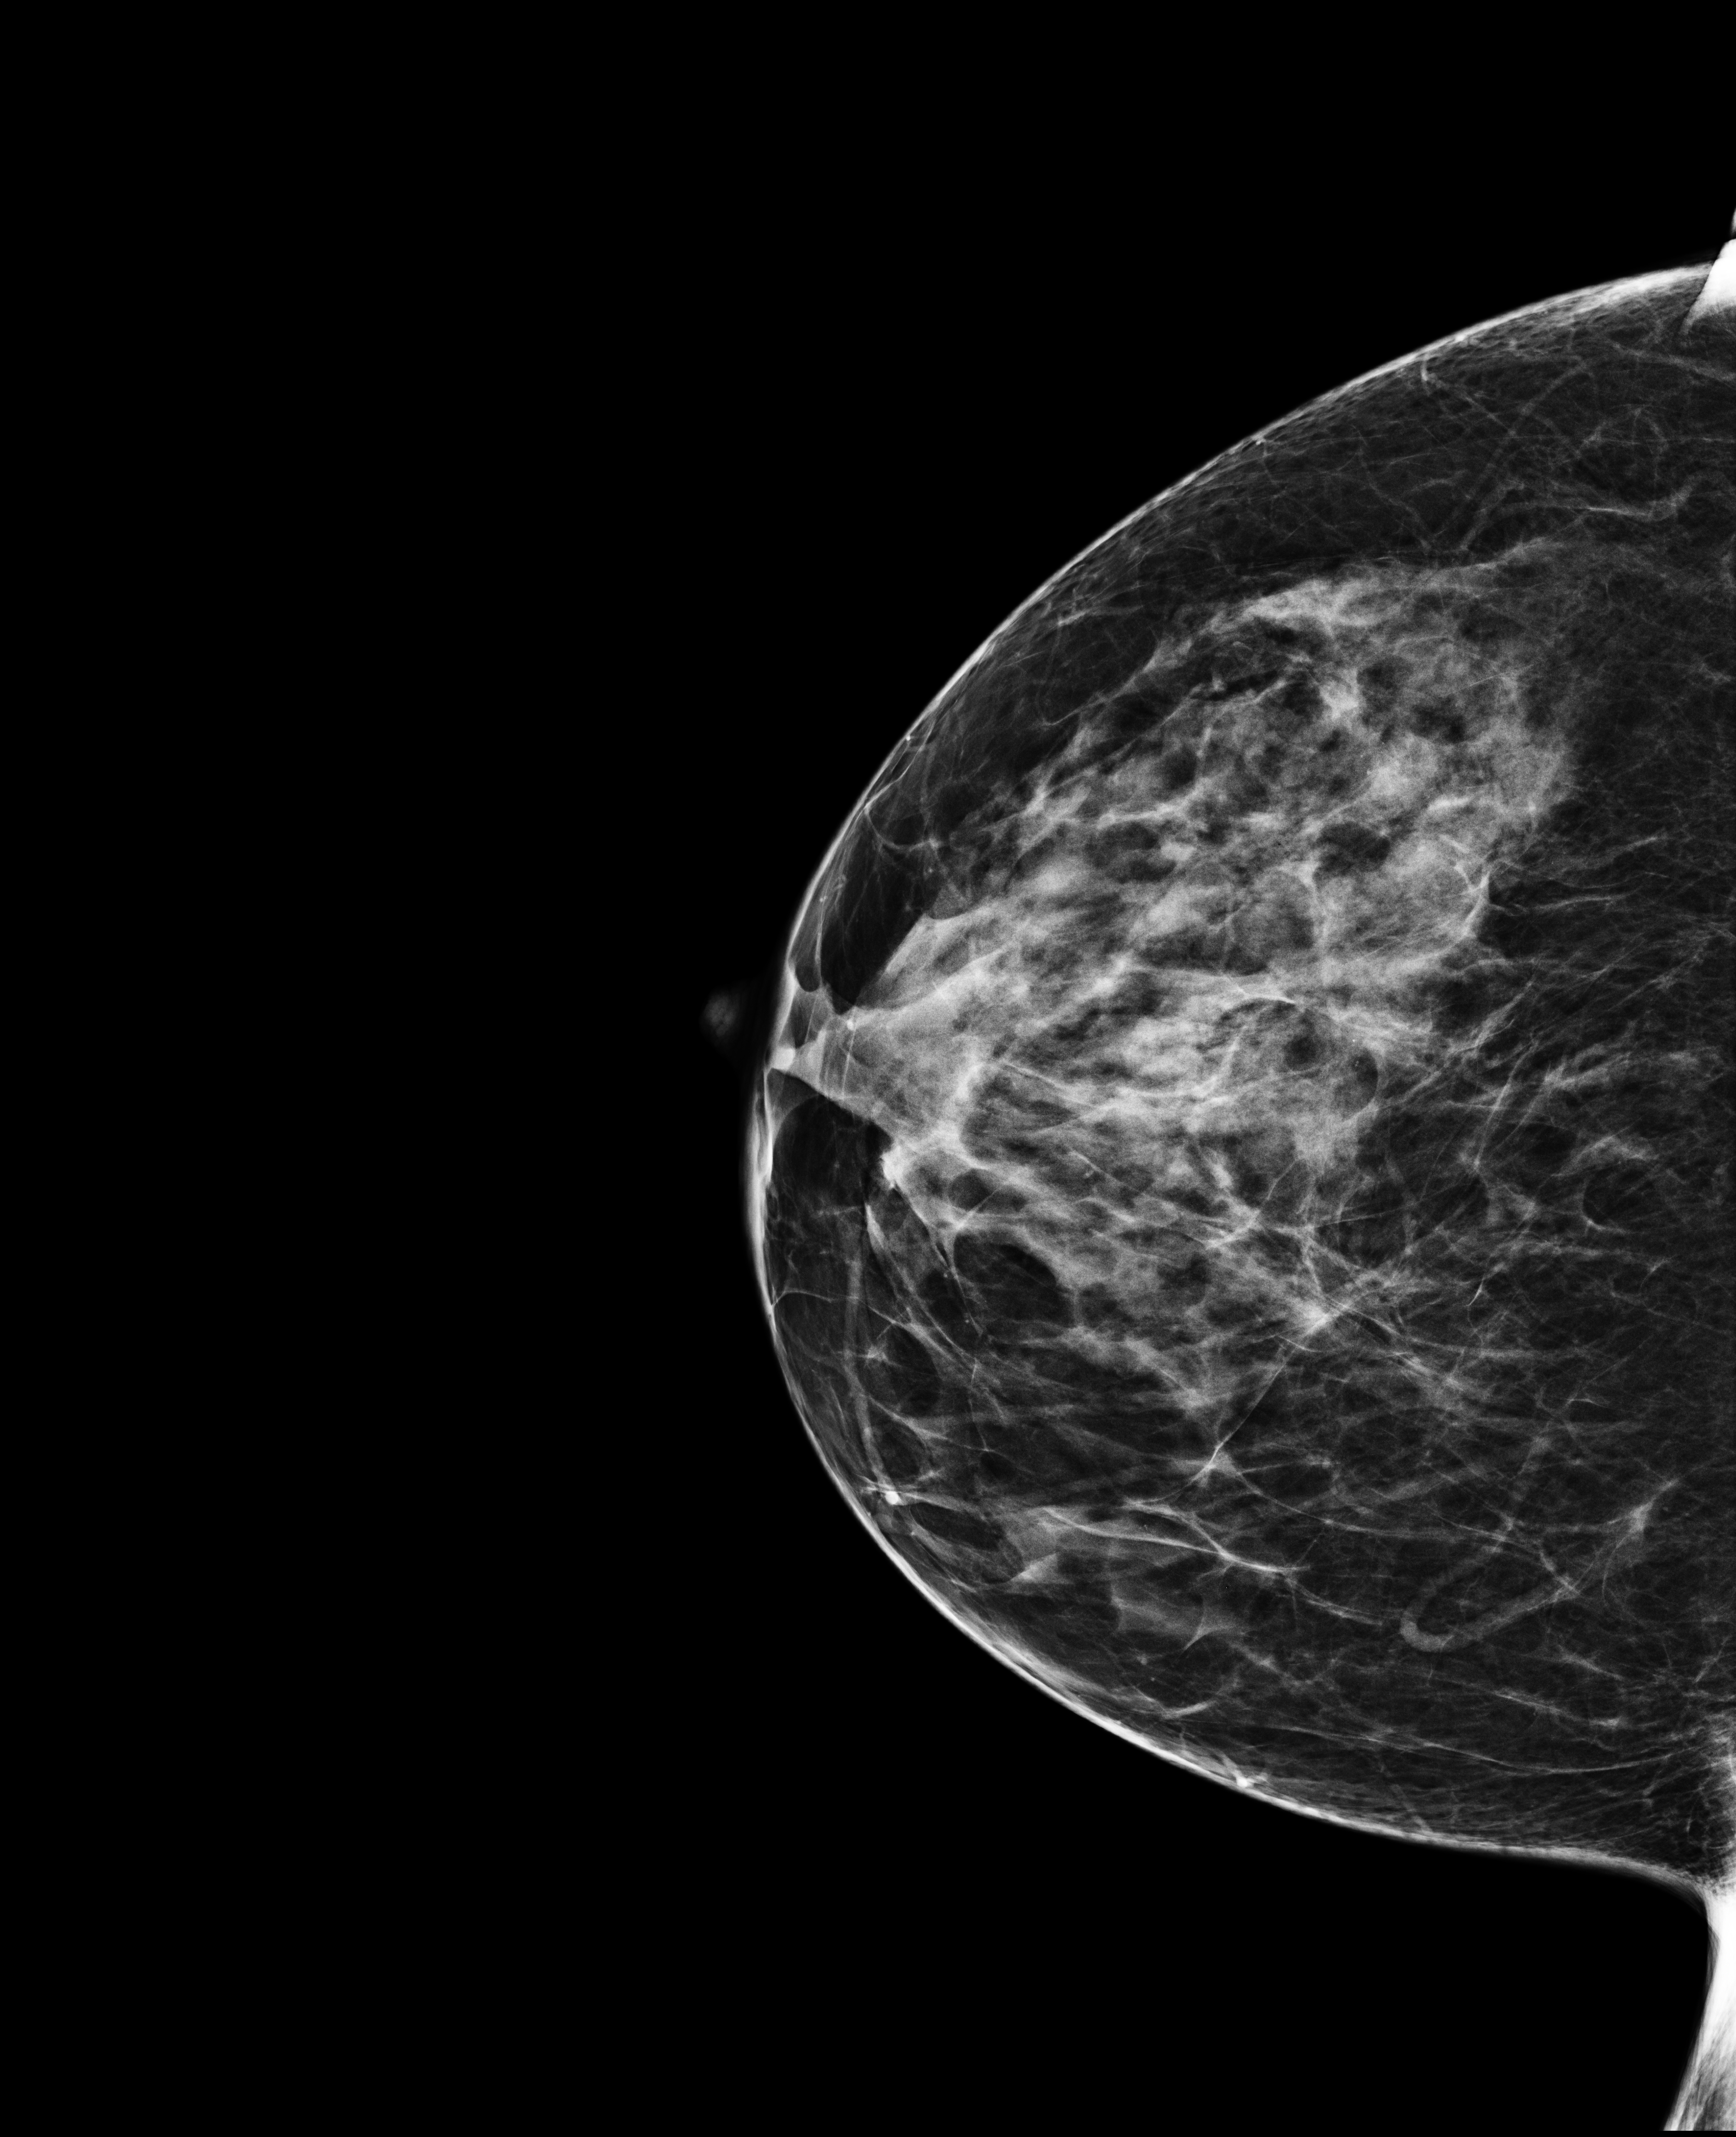
Digital mammogram (FFDM); right breast; craniocaudal (CC) view; annual screening mammography examination; compressed breast thickness 53 mm. Female patient, age 53 years.
Breast density at the screening exam (both breasts): scattered fibroglandular densities (BI-RADS density category b). Final BI-RADS category for the screening round (tomosynthesis exam, both breasts): category 1. Recall: no recall after this screen.